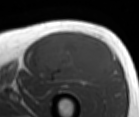
MRI of an extremity soft-tissue mass, one axial slice; slice 54 of 86 in the series (ordered by position); MR volume resampled by the dataset authors to the PET/CT grid (not the native acquisition matrix); 3.27 mm slice thickness; 139 × 117 image matrix, field of view 136 × 114 mm. Male patient. Case-level facts recorded for this patient, not image findings: histological type: extraskeletal osteosarcoma; grade: high; site of the primary tumour: thigh.
Outlined on this slice (expert contour drawn on MRI and transferred to this co-registered scan by the dataset authors):
- gross tumour volume (mass): bounding box (x1, y1, x2, y2) in pixels: (36, 32, 112, 83)